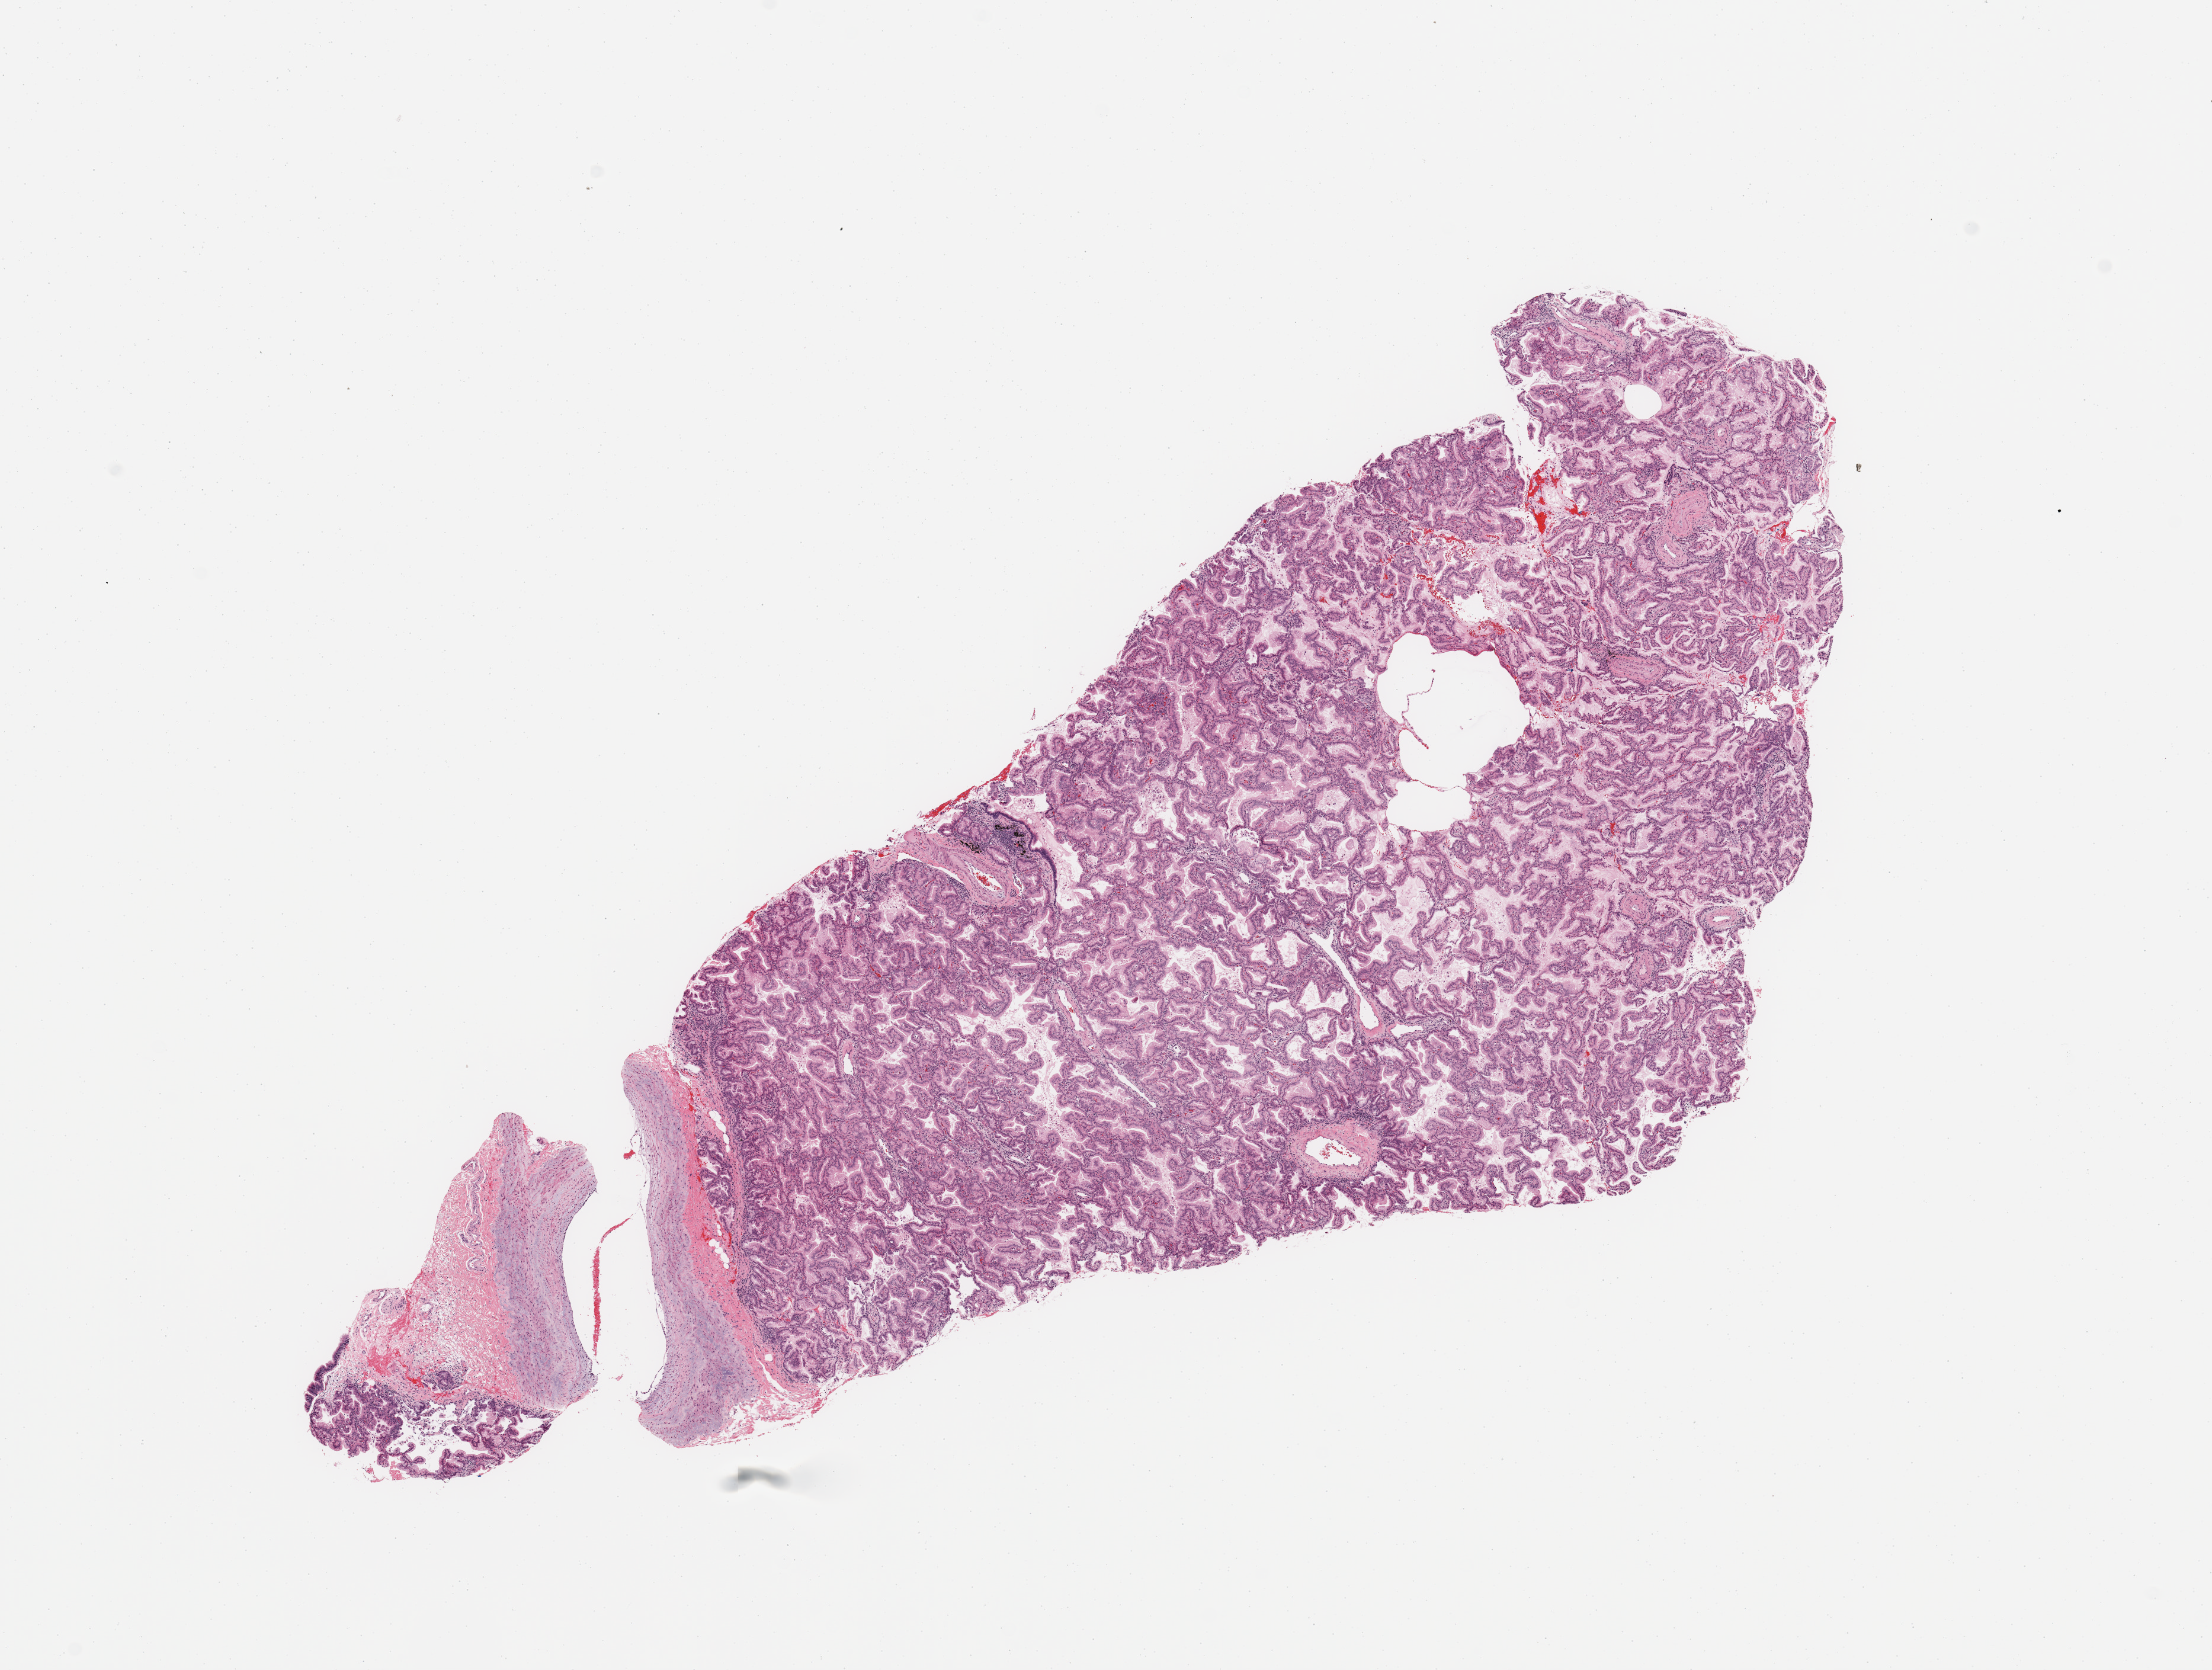
H&E-stained whole-slide image, low-resolution overview of the scanned area, about 14.8 x 11.1 mm; tumour tissue sample, sampled site: lung. 69-year-old male patient. Histologic grade: G1 (well differentiated). Composition of this section per pathologist review: tumour nuclei 85%, necrosis 0%.
Histologic diagnosis: Adenocarcinoma, NOS. Primary tumour site (as recorded): left lower lobe. AJCC pathologic stage: IIB.